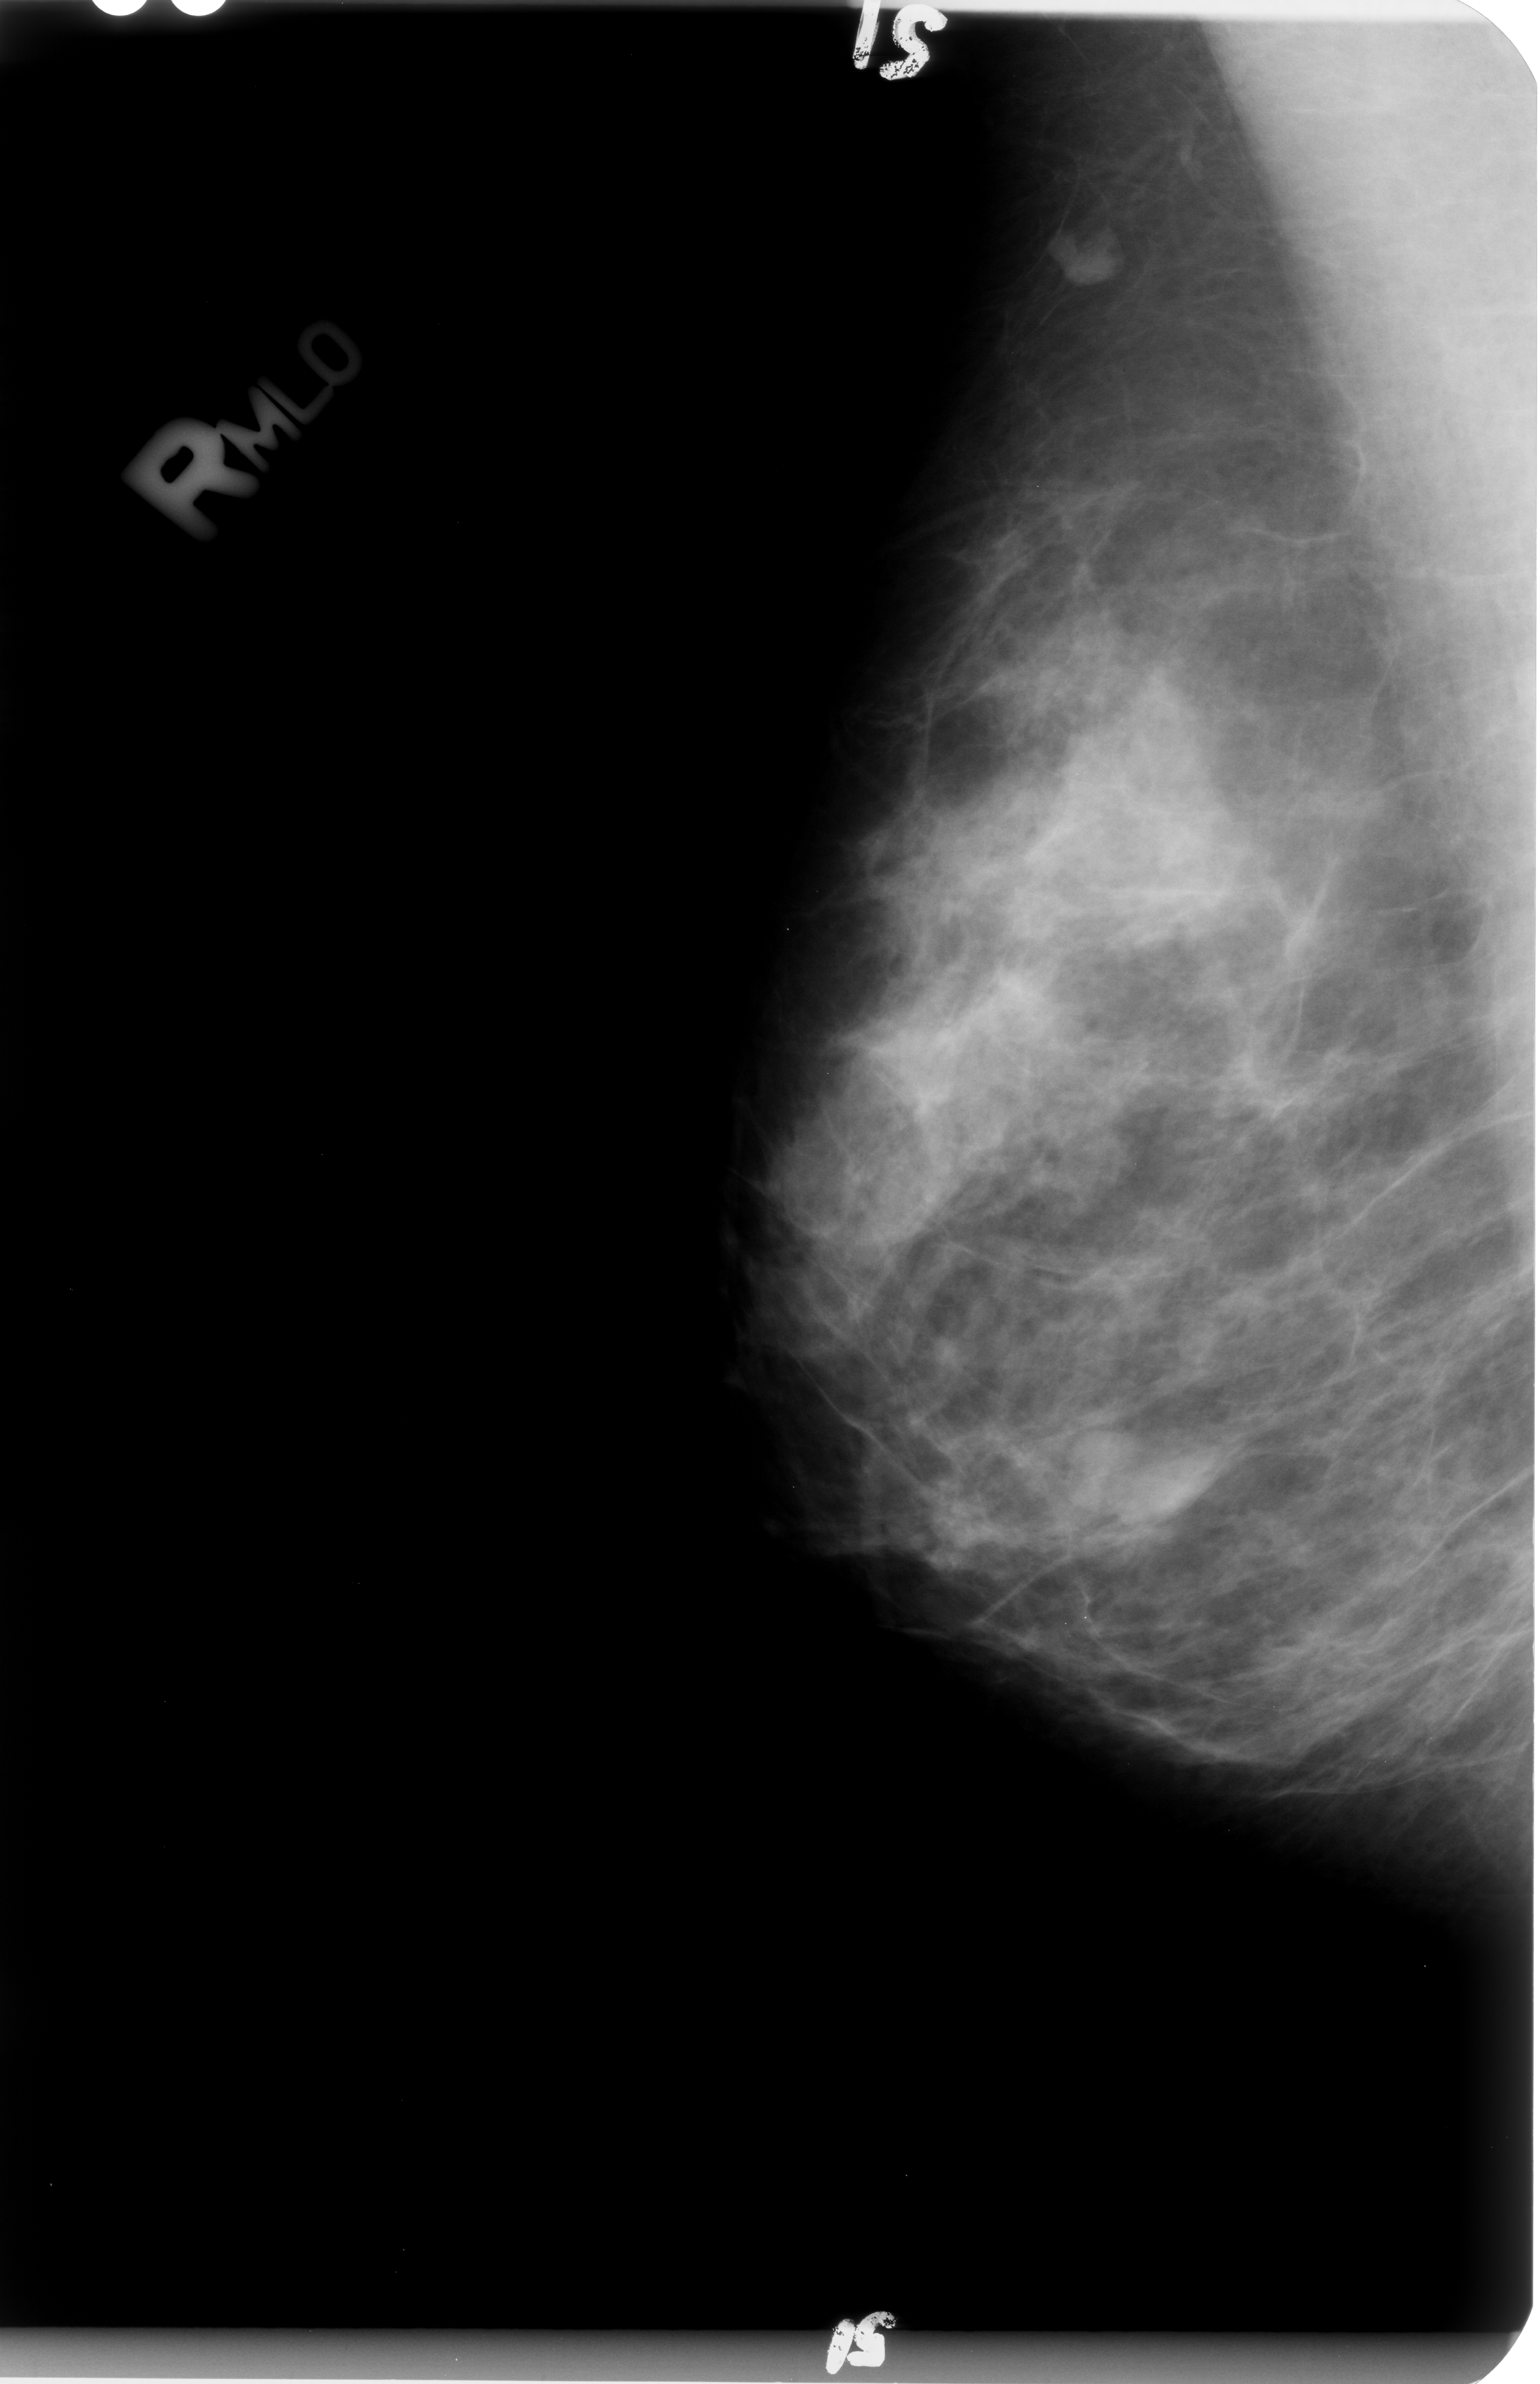
Scanned film-screen mammogram. Right breast. MLO view. Breast composition: heterogeneously dense (BI-RADS density category 3 of 4). 1540 × 2384 image matrix.
Expert-marked regions of interest on this image (one box per marked abnormality):
- mass, shape irregular, margins circumscribed / ill defined; BI-RADS assessment category 4; pathology result (as recorded, not read from the image): benign: box from (x=1078, y=1432) to (x=1219, y=1534) px